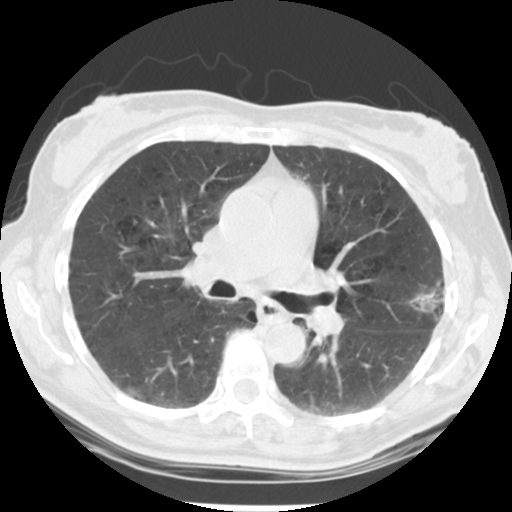
Low-dose screening chest CT, axial slice; second screening round (one year after baseline); lung window (W 1500 / L -600 HU); 2.5 mm slice thickness; standard (soft-tissue) reconstruction kernel (STANDARD). Female, age 61 years at enrolment. Current smoker at enrolment.
Expert-annotated lung lesion, bounding box (x1, y1, x2, y2) in pixels: (403, 274, 464, 334). The exam's reader record, not a measurement of the box and not confirmed to be the same lesion: non-calcified nodule or mass ≥4 mm, left upper lobe, 15 × 15 mm, poorly defined margins, mixed attenuation, pre-existing on the prior screen: no. Official screen result: positive, other. Participant outcome: lung cancer diagnosed 152 days after this screen — bronchiolo-alveolar adenocarcinoma, NOS, left upper lobe, well differentiated (G1), stage IA (AJCC 6th edition), 11 mm at pathology.